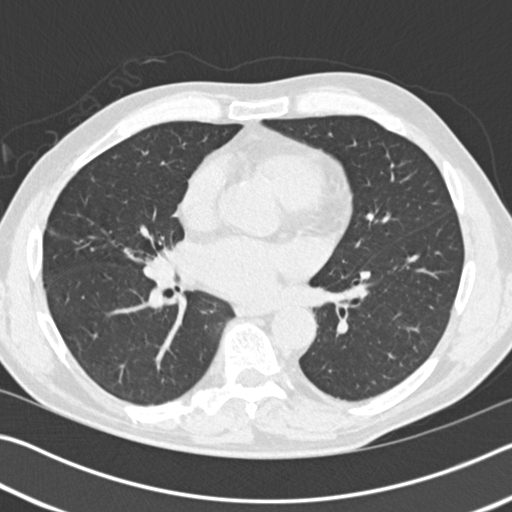
Low-dose screening chest CT, axial slice. Baseline screening round. Lung window (W 1500 / L -600 HU). 2 mm slice thickness. Standard (soft-tissue) reconstruction kernel (B30f). 120 kVp. Slice 89 of 193 in the series. 512 × 512 image matrix. Male participant, aged 57 years at enrolment. Former smoker at enrolment.
Expert reader's lesion annotation, bounding box <143,248,180,283> (left, top, right, bottom; pixels). The screening reader recorded 2 non-calcified nodules or masses ≥4 mm on this exam (right middle lobe, right middle lobe); which of them this box marks is not recorded. Lung cancer was diagnosed 784 days after this screen (after the third annual screen): carcinoid tumor, NOS, right middle lobe, carcinoid, stage not assessed, 15 mm at pathology.